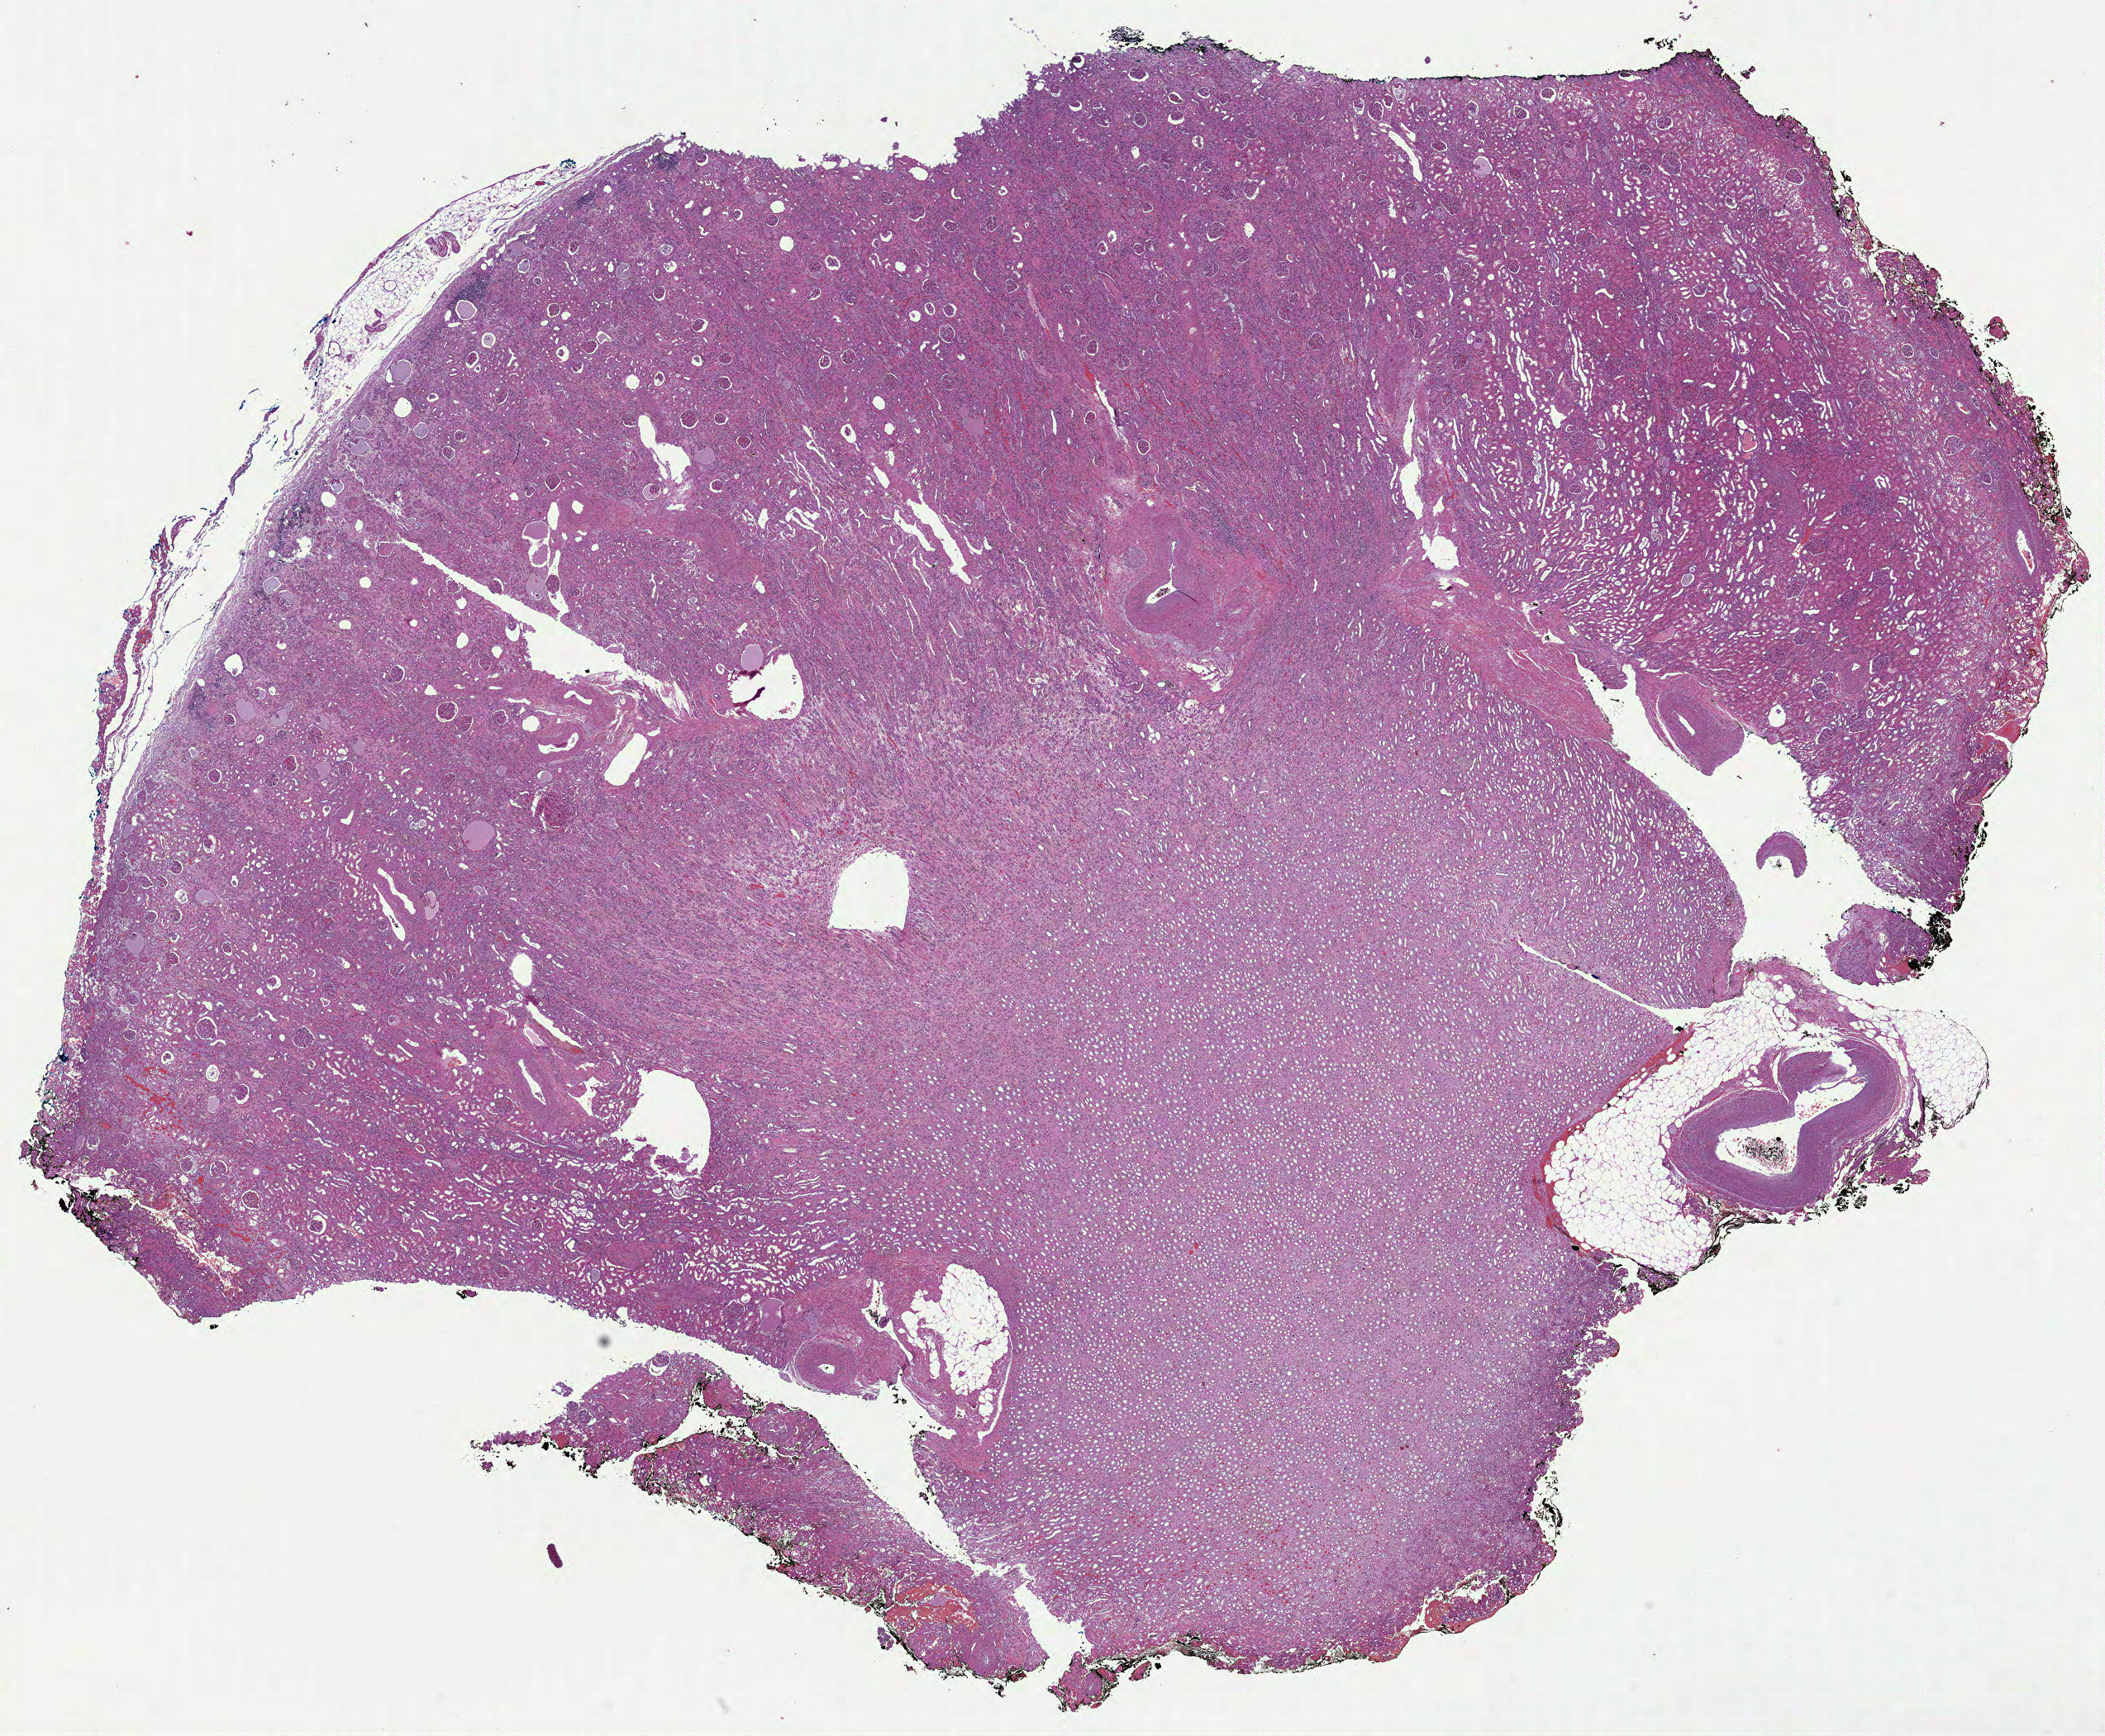
Digitized Hematoxylin and eosin (H&E) stained tissue section (whole slide) — whole scanned area (about 20.5 x 16.9 mm) shown as a low-resolution overview. Formalin-fixed paraffin-embedded (FFPE) diagnostic section. Kidney, primary tumour sample. Patient: male, age at initial diagnosis 75 years. Histologic grade: G2 (moderately differentiated).
Histologic diagnosis: Clear cell adenocarcinoma, NOS. Laterality: right. AJCC pathologic stage: I.